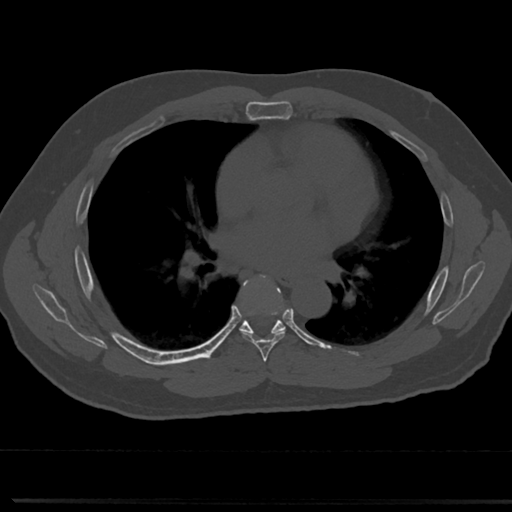
CT including the spine, one axial slice. Position 433 of 817 along the scan axis. Bone window (W 1800 / L 400 HU). 512 × 512 image matrix, field of view 355 × 355 mm. Male patient, age 61 years. From the clinical record (not read from this slice): primary cancer: prostate.
Structures marked on this image (semi-automatic segmentation, software-assisted and operator-edited):
- T5 vertebra: bounding box (x1, y1, x2, y2) in pixels: (265, 370, 272, 377)
- T6 vertebra: (237, 276, 291, 355)
- T7 vertebra: (242, 327, 282, 333)